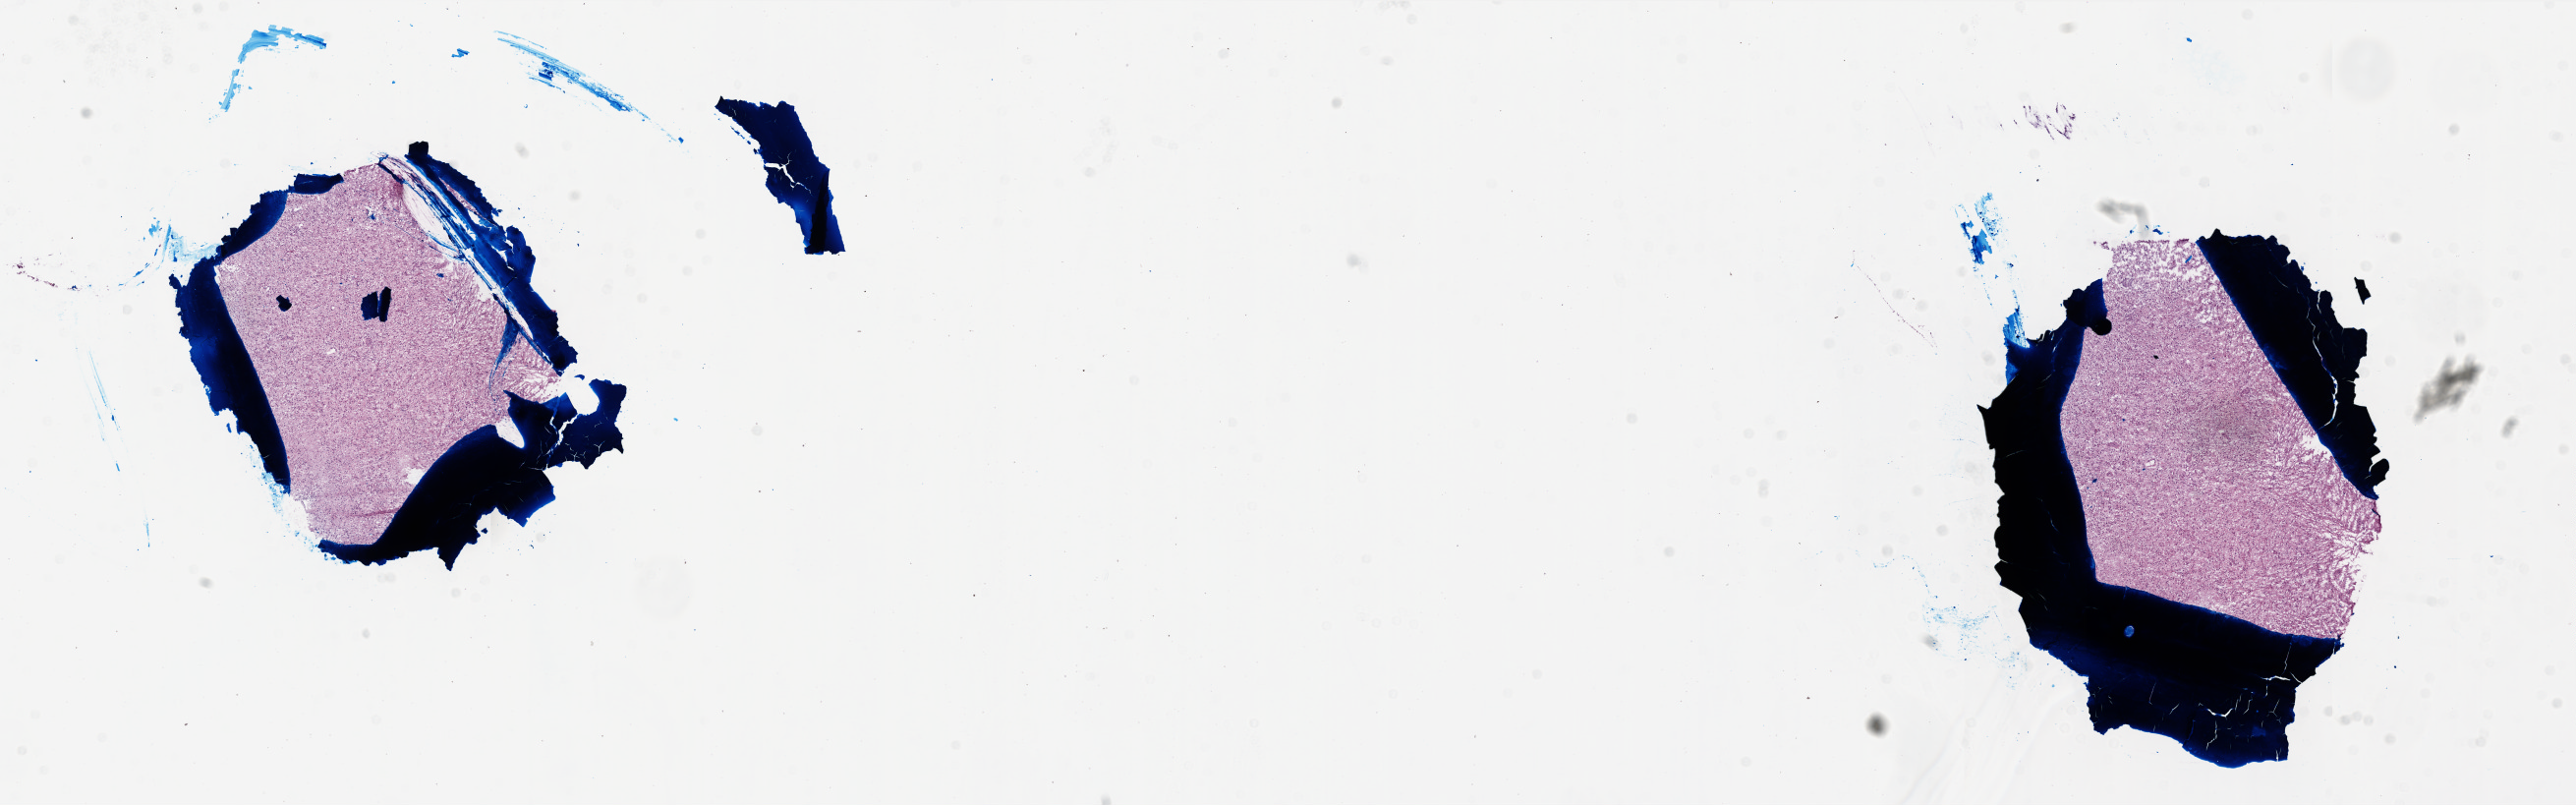
Whole-slide histology image, H&E, low-resolution overview of the scanned area, about 21.0 x 6.6 mm, frozen section from the top of the tissue portion, primary tumour sample from the brain. Patient: male, age at initial diagnosis 67 years. Slide review estimates, as recorded: tumour cells 95%, tumour nuclei 100%, normal cells 0%, stromal cells 0%, necrosis 5%.
- pathologic diagnosis: Glioblastoma